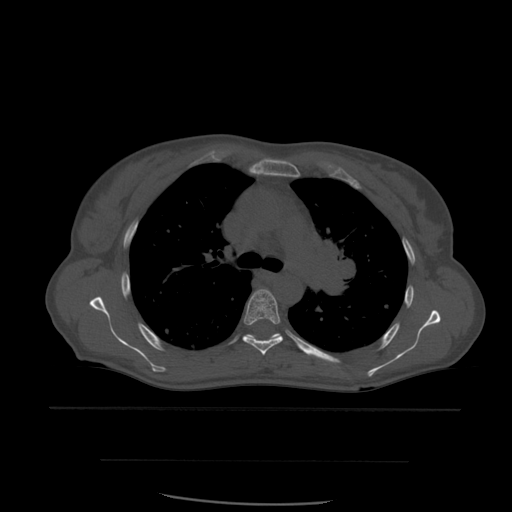
CT including the spine, one axial slice. Slice 408 of 574 in the series (ordered by position). Bone window (W 1800 / L 400 HU). 1.25 mm slice thickness. 512 × 512 image matrix, field of view 392 × 392 mm. Patient age 48 years. Case-level facts recorded for this patient, not image findings: primary cancer: lung; vertebrae with lytic lesions (as recorded): T11.
Outlined on this slice (semi-automatic segmentation, software-assisted and operator-edited):
- T5 vertebra: box from (x=243, y=289) to (x=283, y=356) px
- T6 vertebra: (x=244, y=333)–(x=281, y=341)